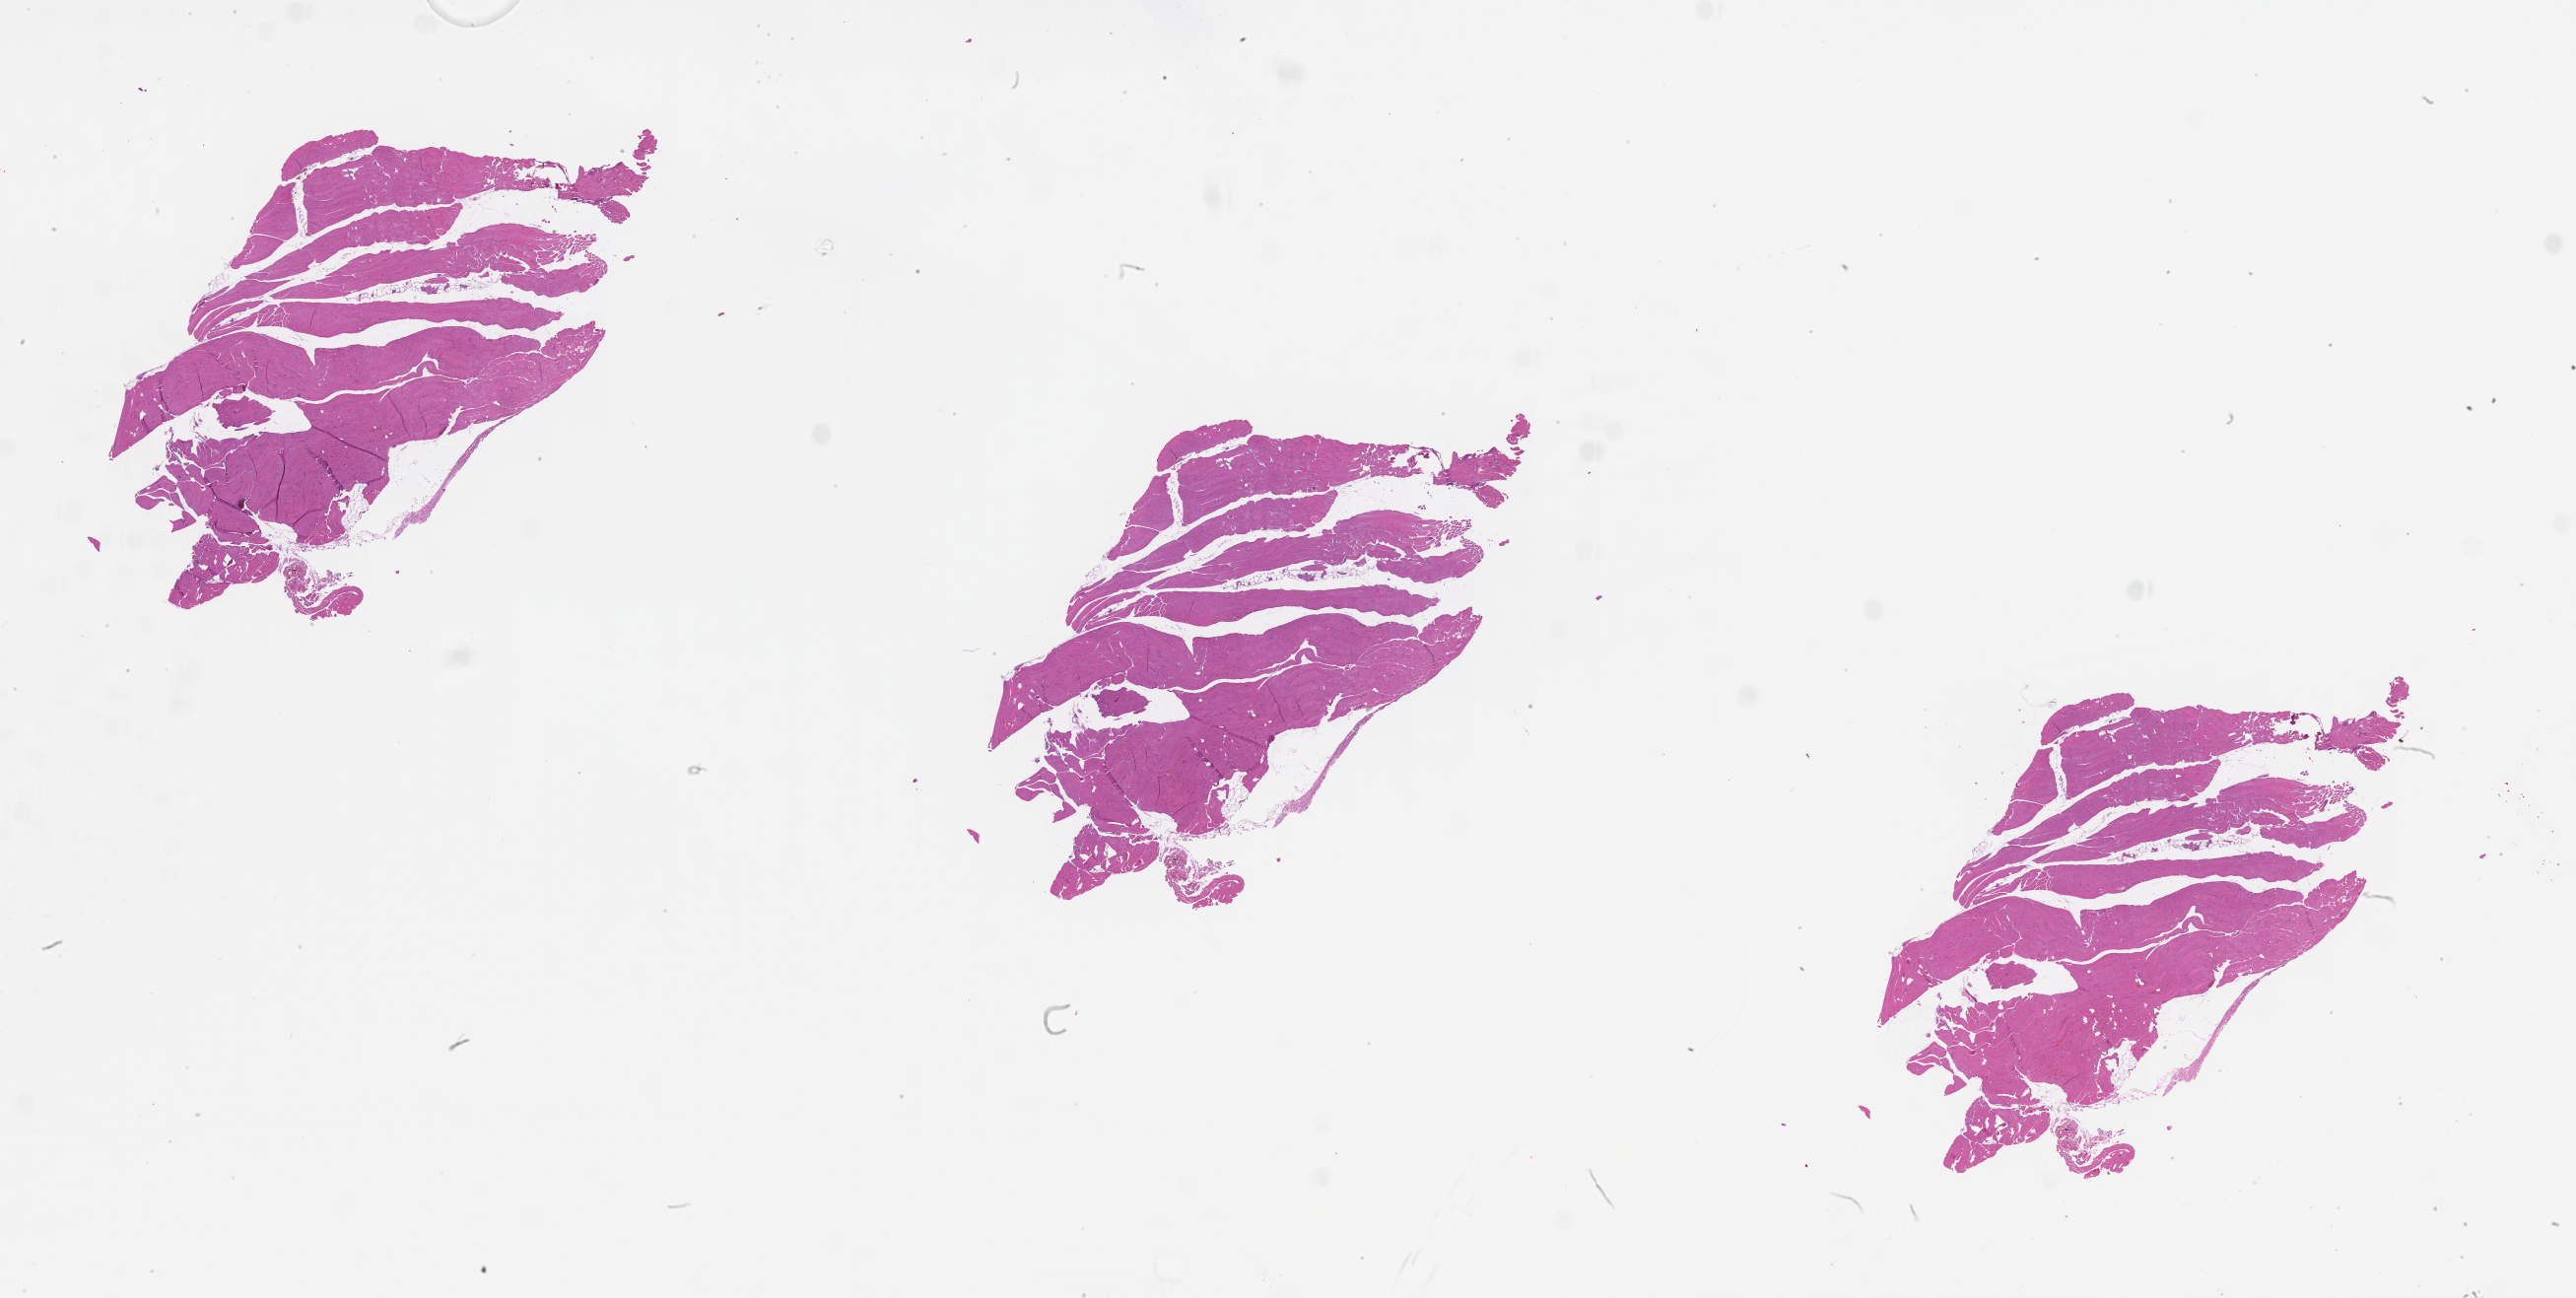
Digitized Hematoxylin and eosin (H&E) stained tissue section (whole slide) — whole scanned area (about 42.1 x 21.2 mm, from a 20x scan) shown as a low-resolution overview.
Patient diagnosis (cohort enrolment): sarcoma (site not recorded at cohort level).